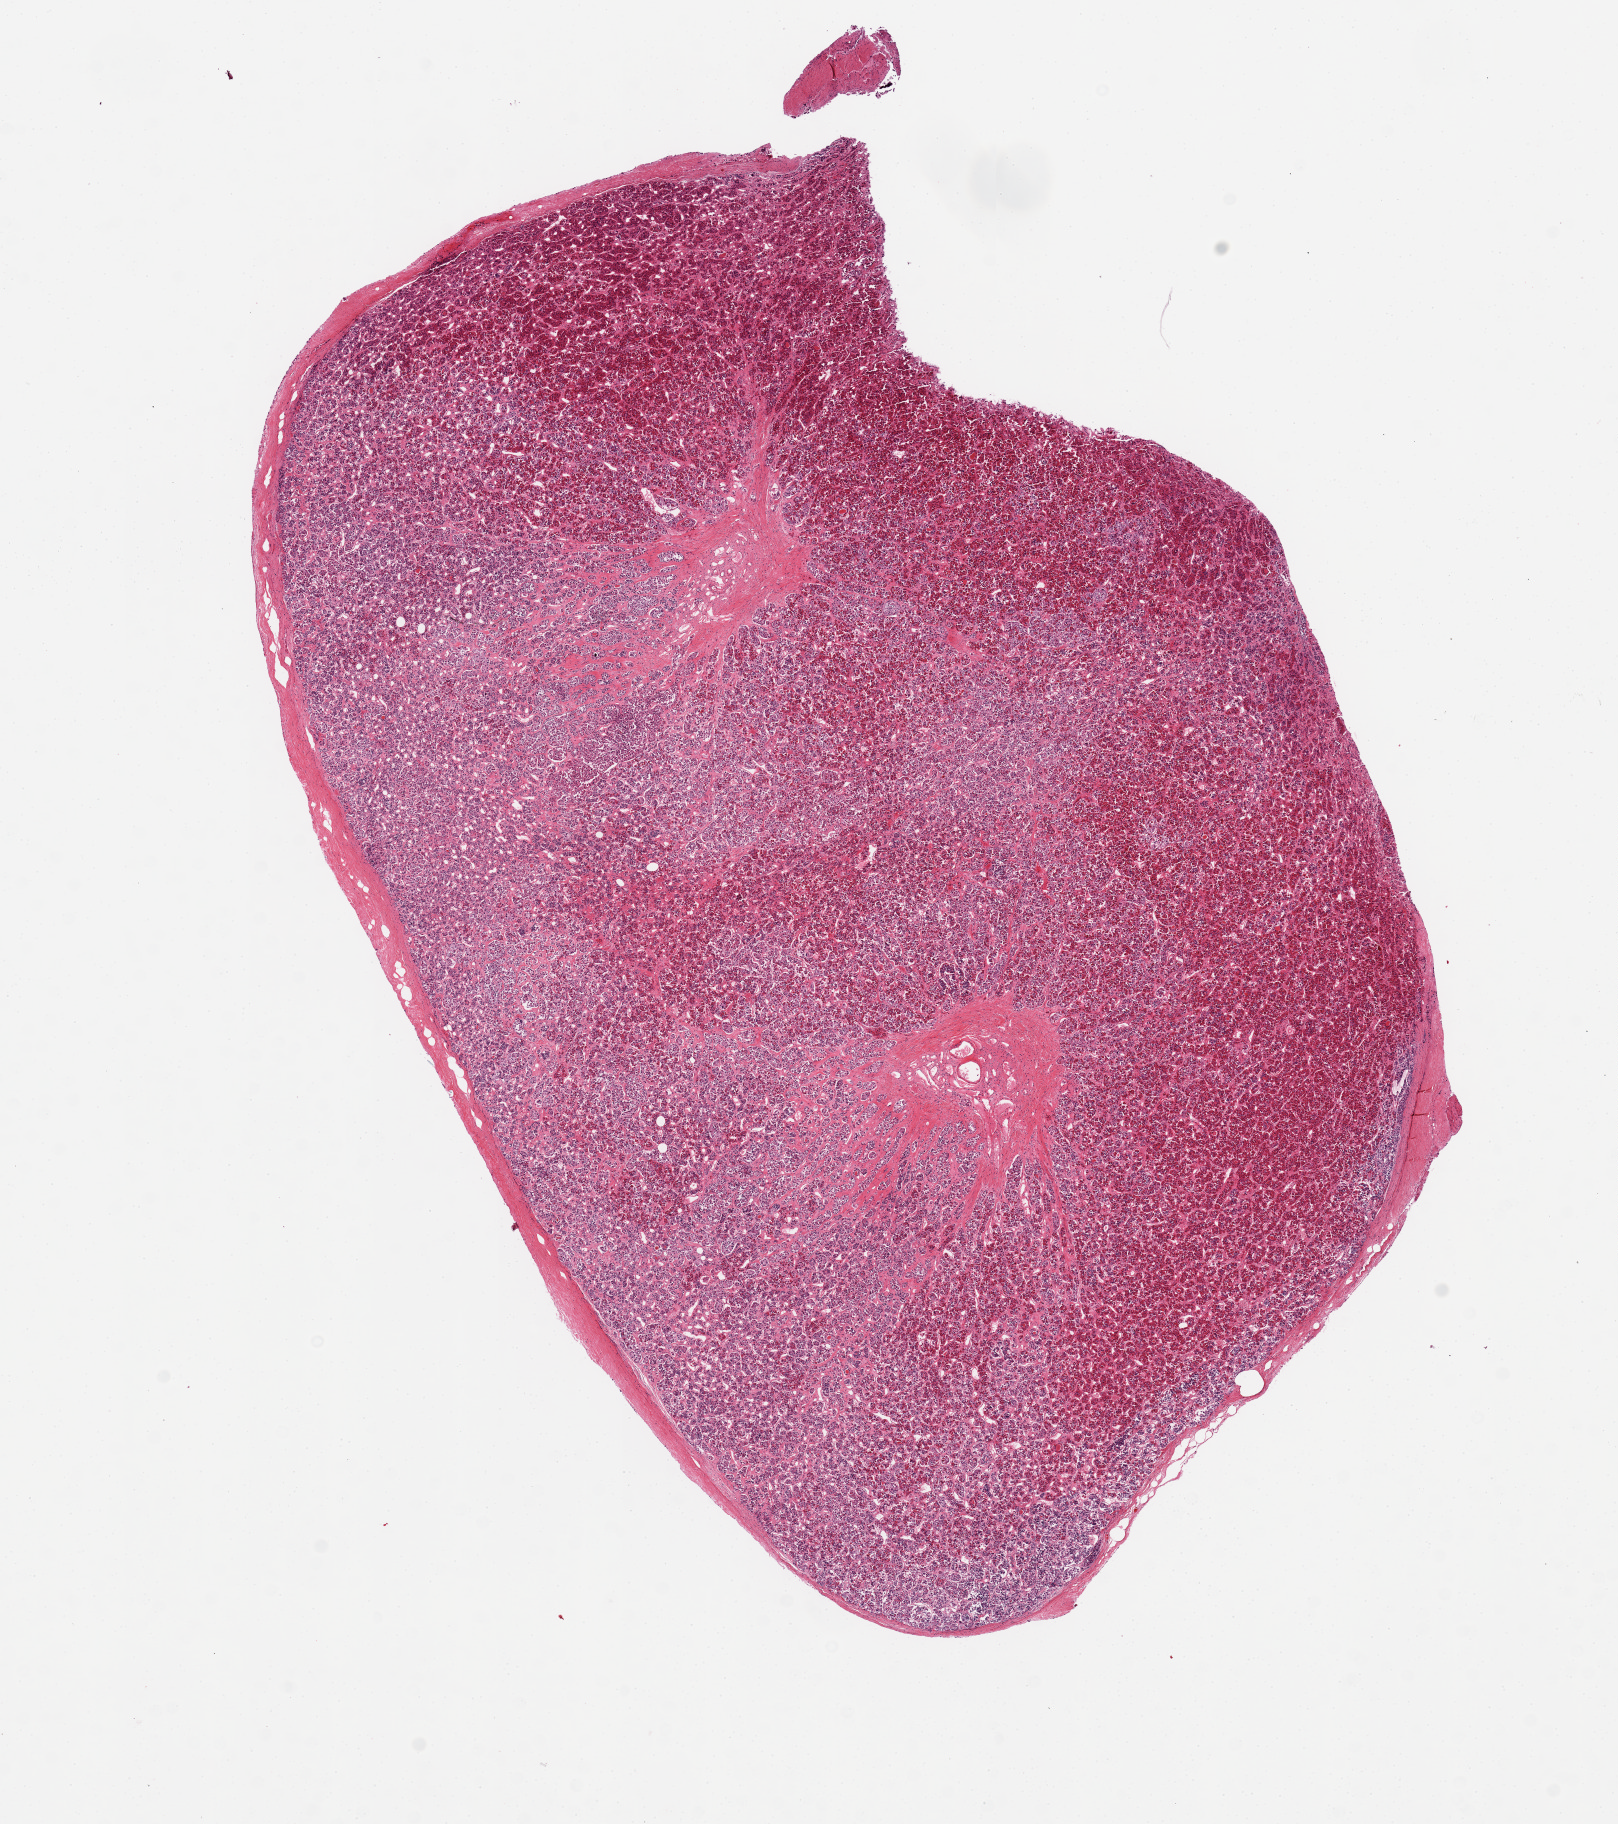
Digitized H&E-stained section, shown as a low-resolution overview of the whole scanned area (about 12.8 x 14.4 mm, from a 20x scan). PAXgene-fixed, paraffin-embedded tissue. Sampled site (target tissue): pituitary. Tissue donor sample. Donor sex: male.
• pathologist's review note for this sample: 1 piece, adenohypophysis